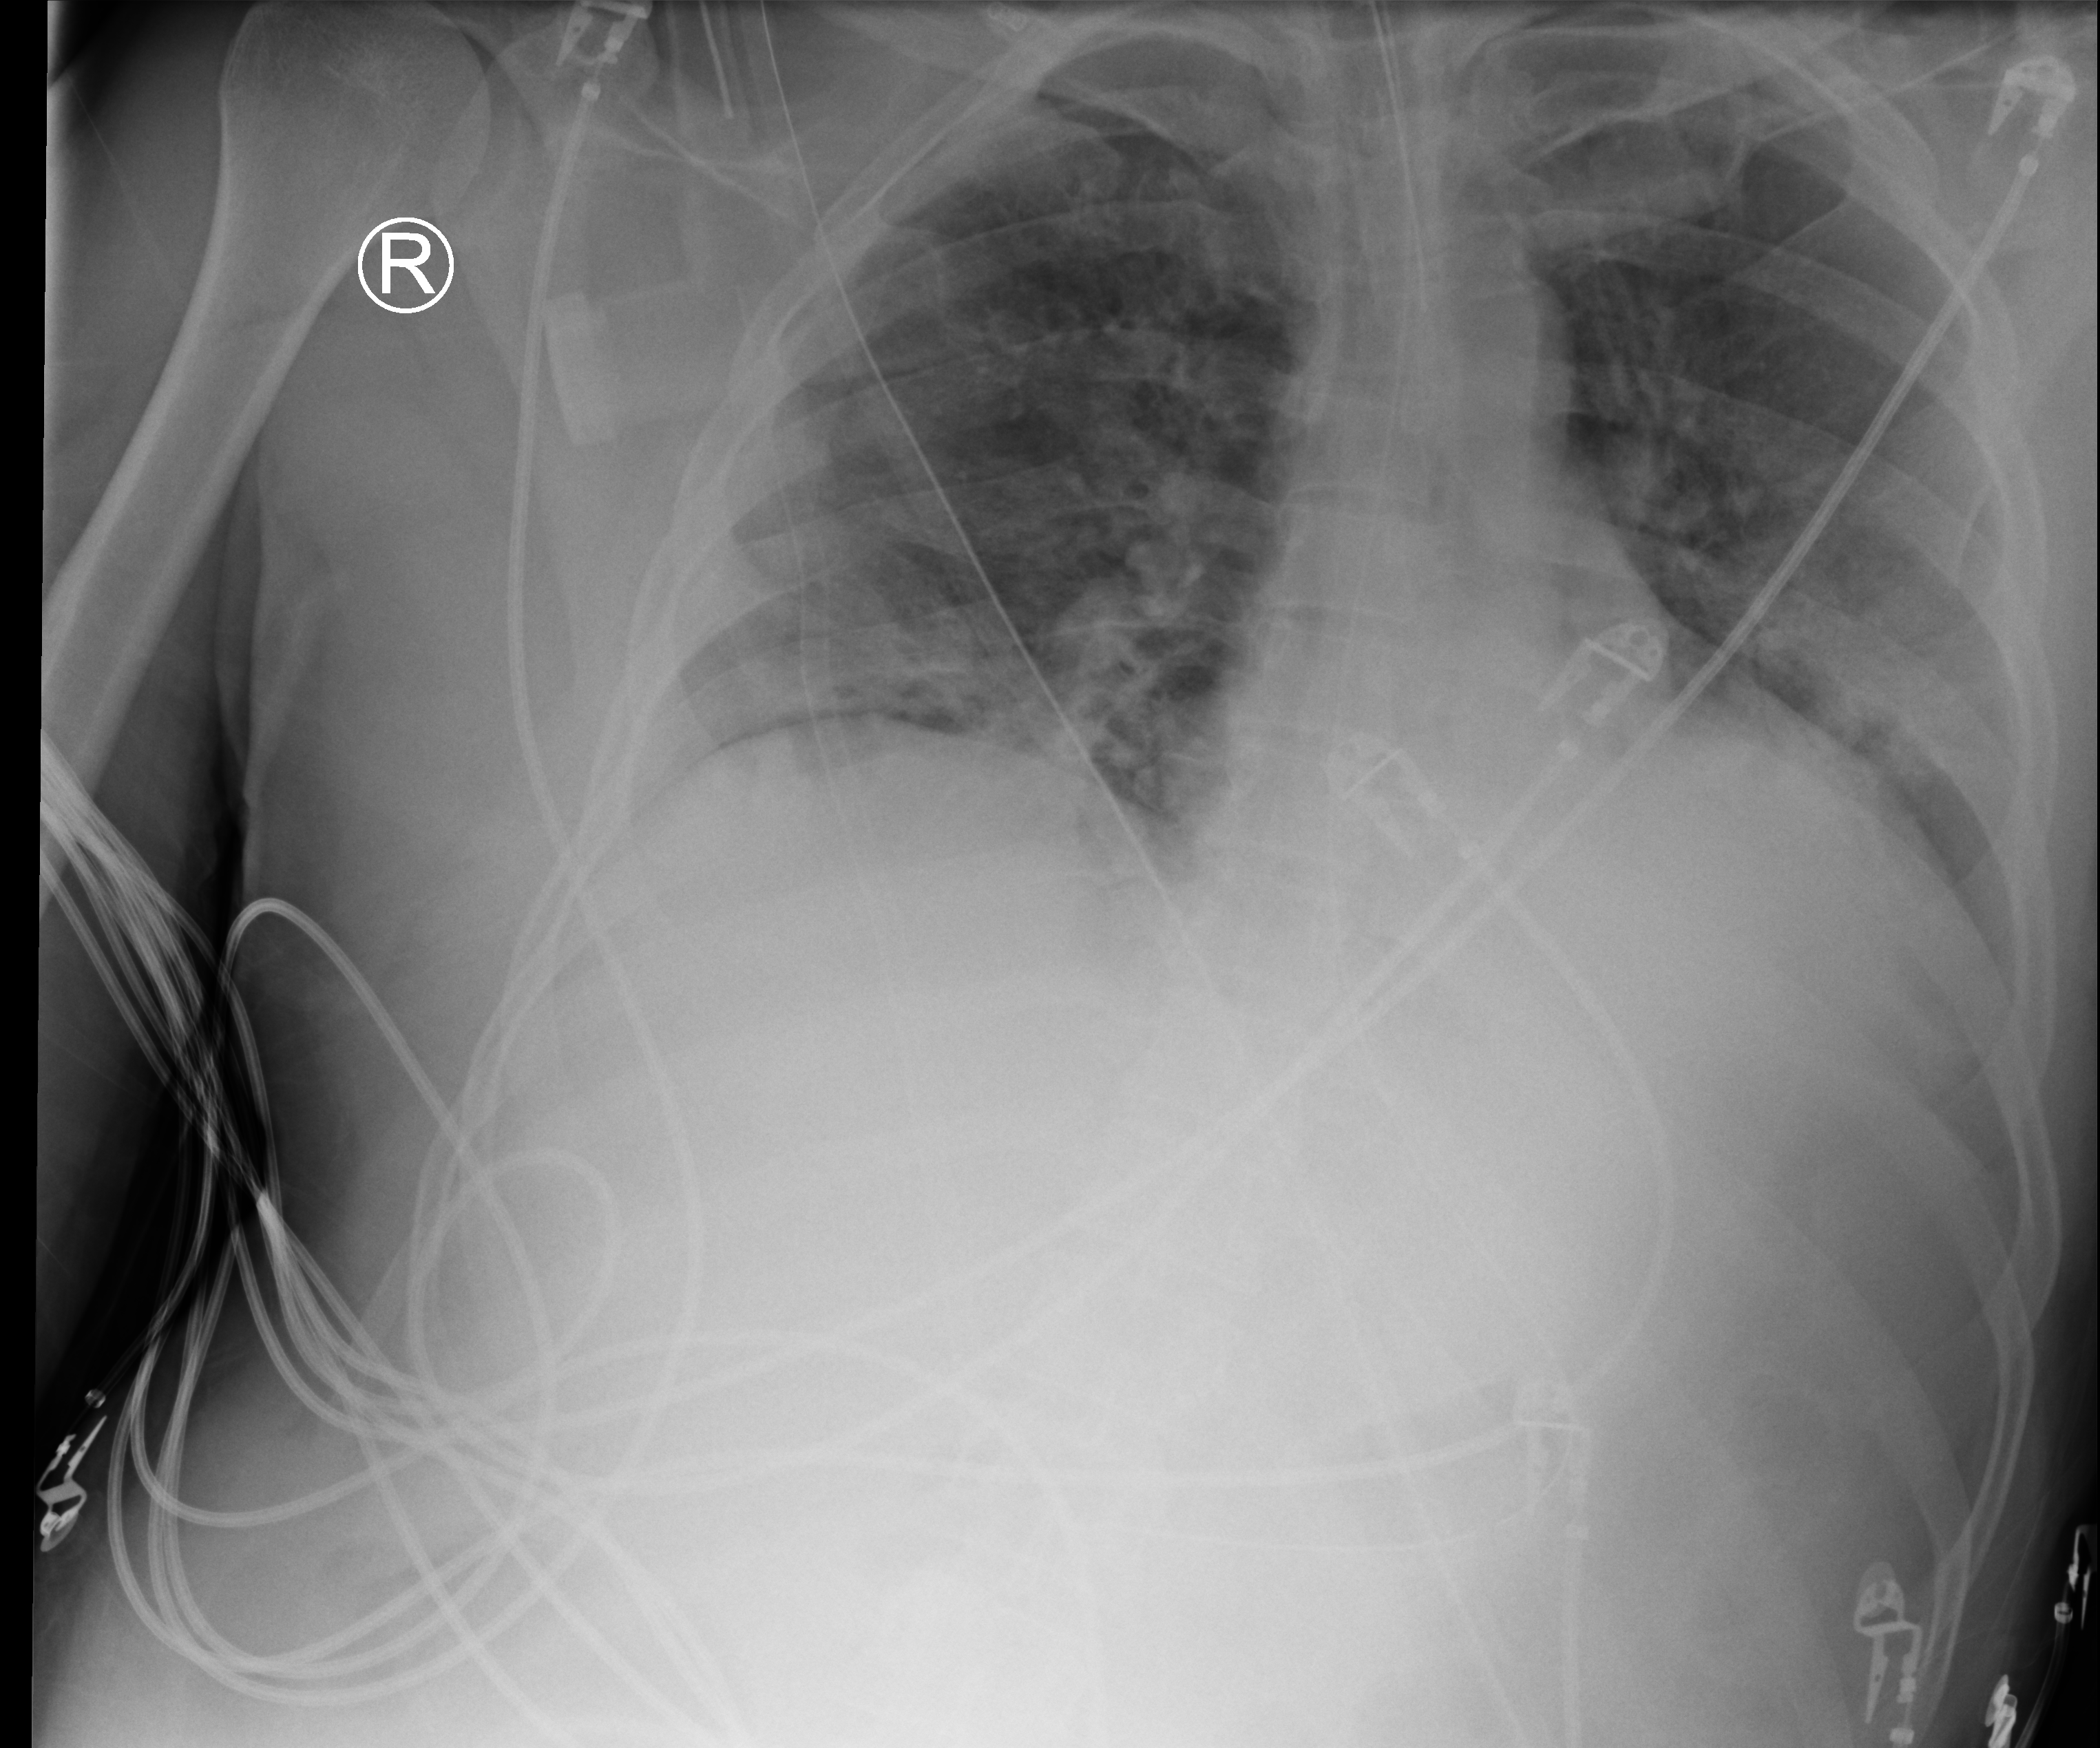
Bedside chest radiograph (computed radiography); anteroposterior (AP) projection. Patient hospitalised with COVID-19; male, aged 18–59 years.
From the hospital-stay record, not from the radiograph (when in the stay this image was taken is not recorded): other chronic lung disease (admission record): no; hypertension (admission record): no.